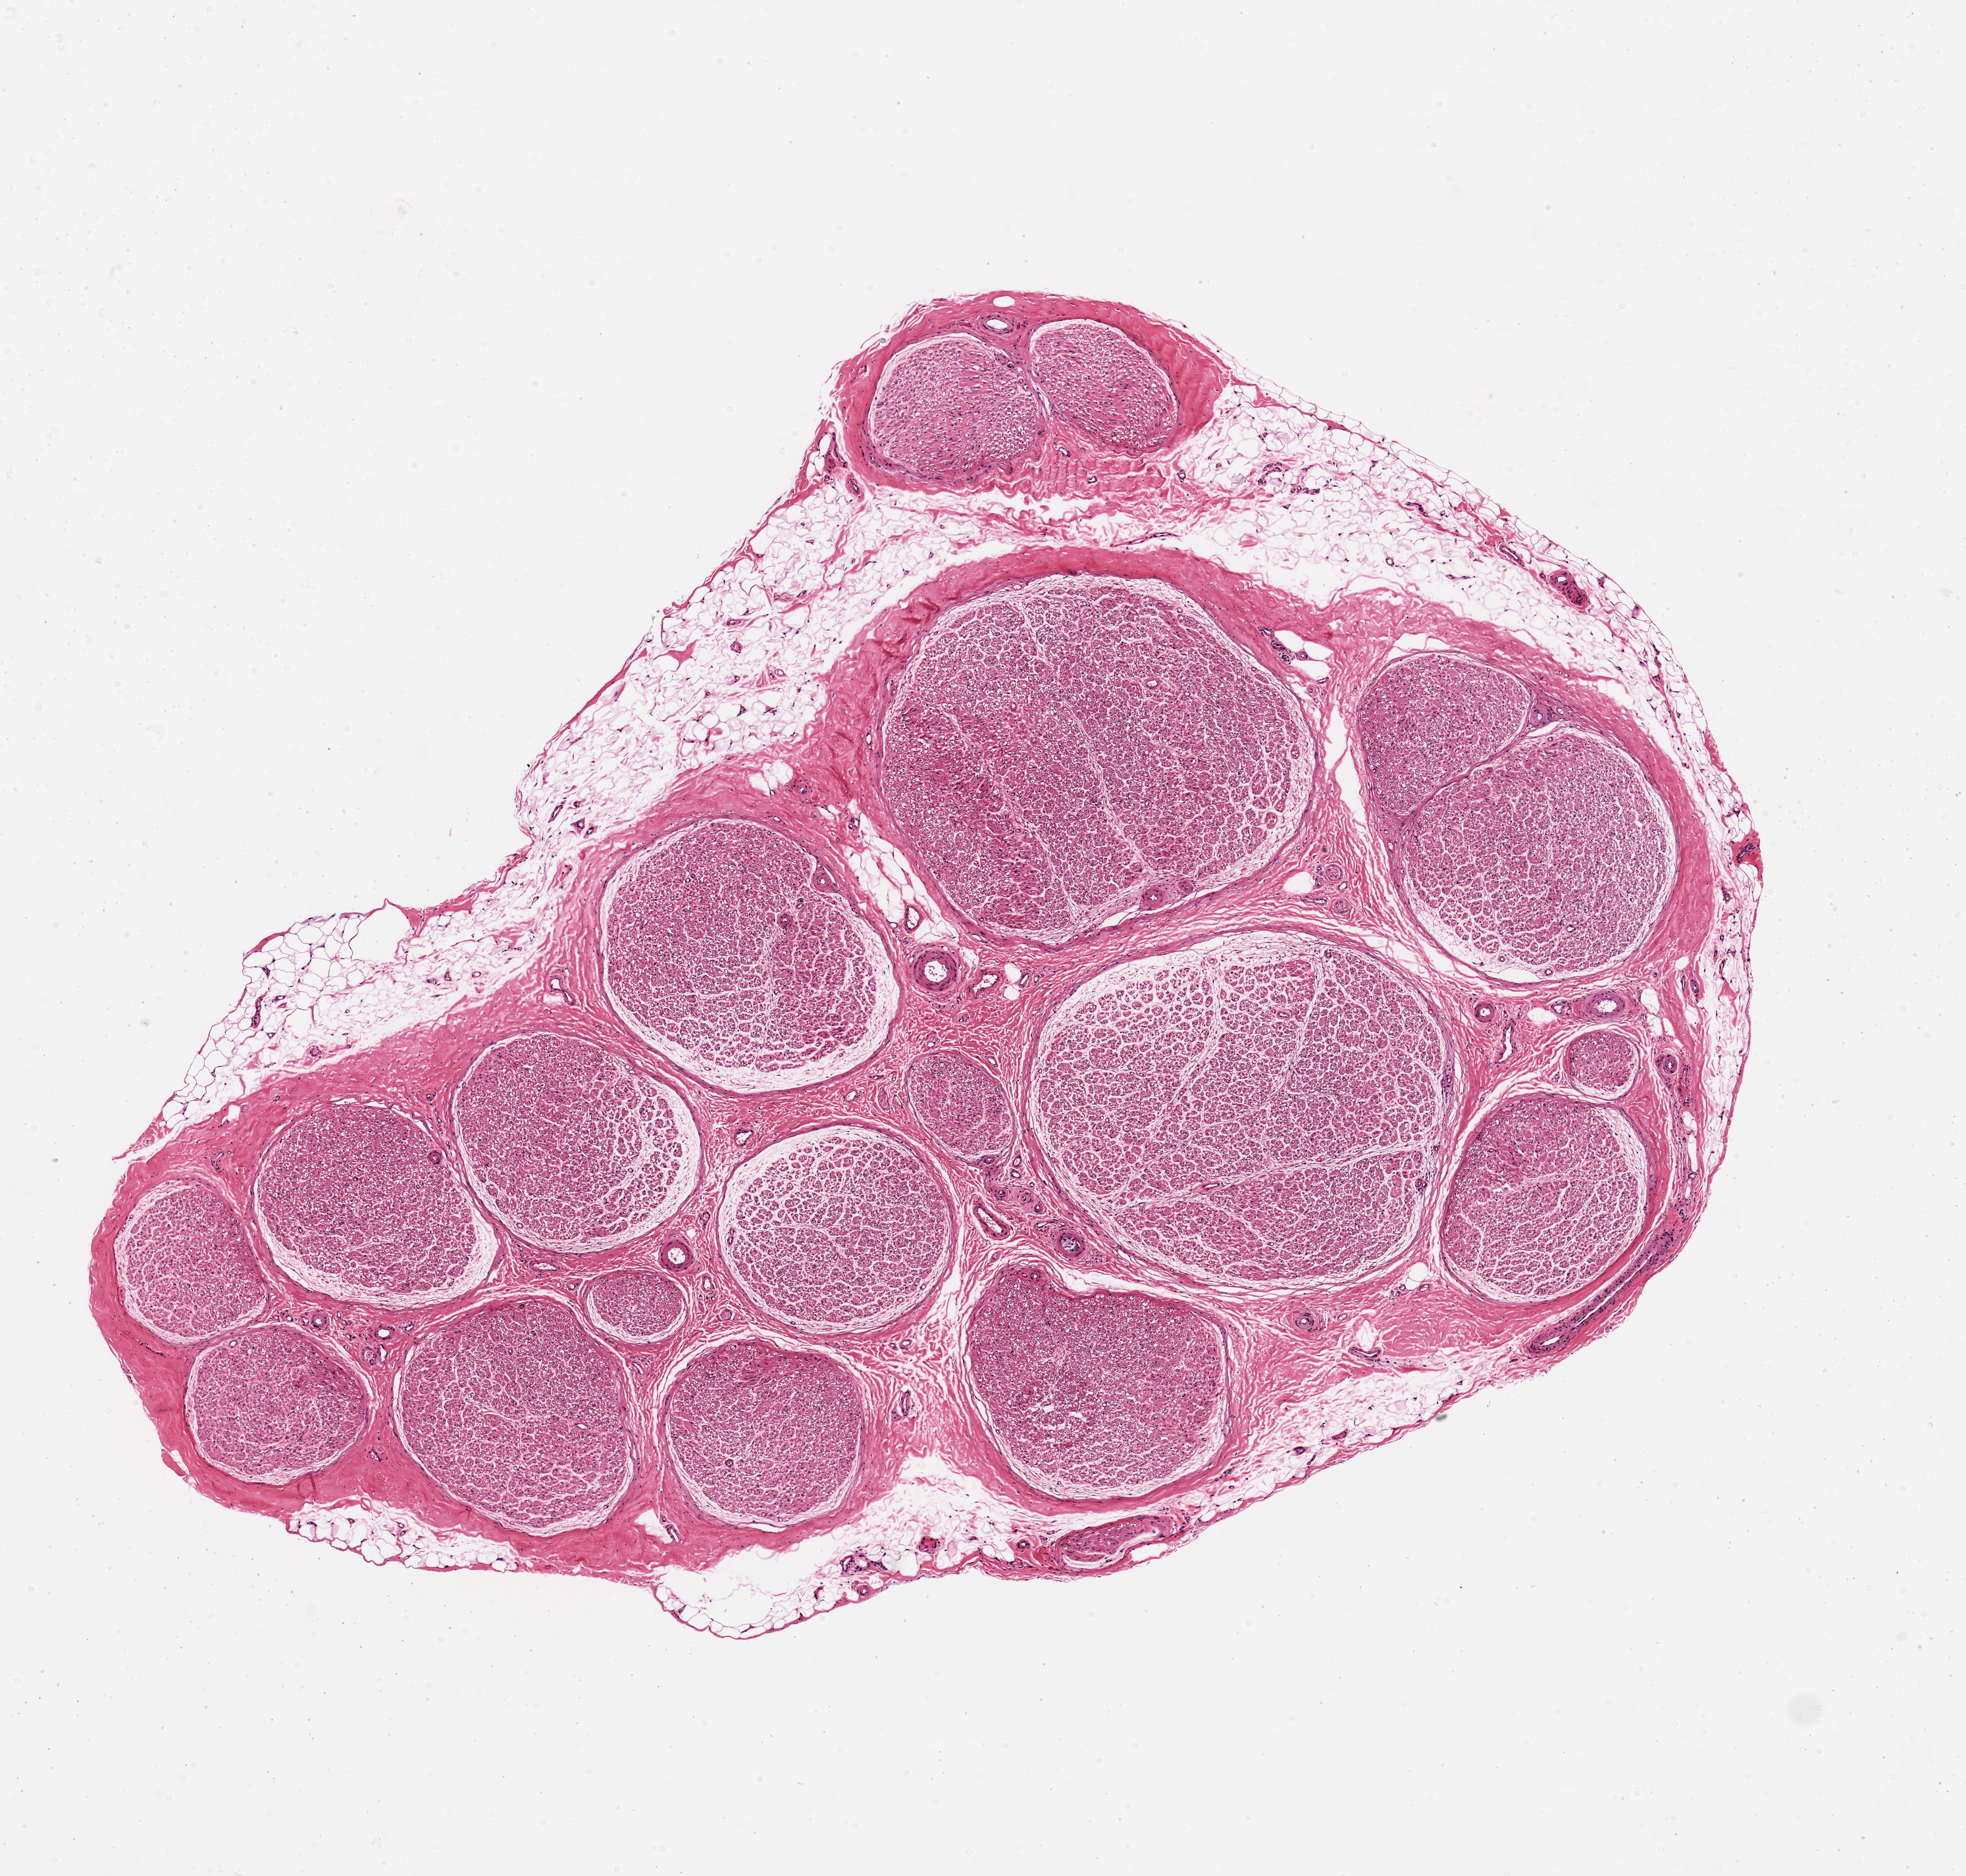
Haematoxylin and eosin whole-slide image — a low-resolution overview of the entire scanned area, about 5.9 x 5.6 mm; PAXgene-fixed, paraffin-embedded tissue; sampled site (target tissue): tibial nerve; donor tissue sample. Donor sex: male.
* review note (as recorded): OK for analysis